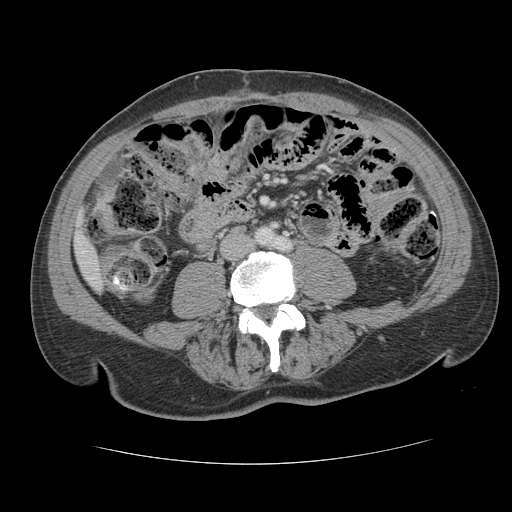
Contrast-enhanced abdominal CT, one axial slice. Position 20 of 134 along the scan axis. Reconstruction kernel STANDARD. 120 kVp. Intravenous contrast given. Soft-tissue window (W 400 / L 40 HU). 2.5 mm slice thickness. 512 × 512 image matrix. Male patient, age 68 years. Case-level facts recorded for this patient, not image findings: diagnosis: colorectal cancer liver metastases, imaged before liver resection; multiple liver metastases: yes; largest metastasis: 2.2 cm; disease in both lobes: no.
Annotated regions visible in this slice (manually delineated by an expert):
- liver: box from (x=76, y=235) to (x=101, y=287) px
- planned liver remnant (the part of the liver to remain after resection): (x=76, y=235)–(x=100, y=287)